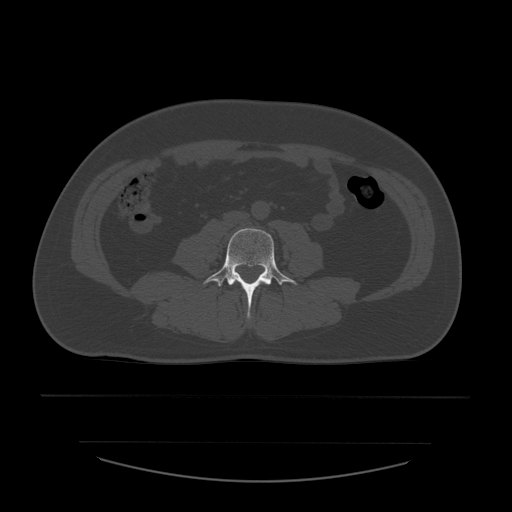
CT including the spine, one axial slice; slice 150 of 532 in the series (ordered by position); 120 kVp; bone window (W 1800 / L 400 HU); 512 × 512 image matrix, field of view 441 × 441 mm. Patient age 44 years. Case-level facts recorded for this patient, not image findings: primary cancer: soft tissue sarcoma.
Structures marked on this image (semi-automatically segmented with operator editing):
- L4 vertebra: bounding box <203,228,298,318> (left, top, right, bottom; pixels)